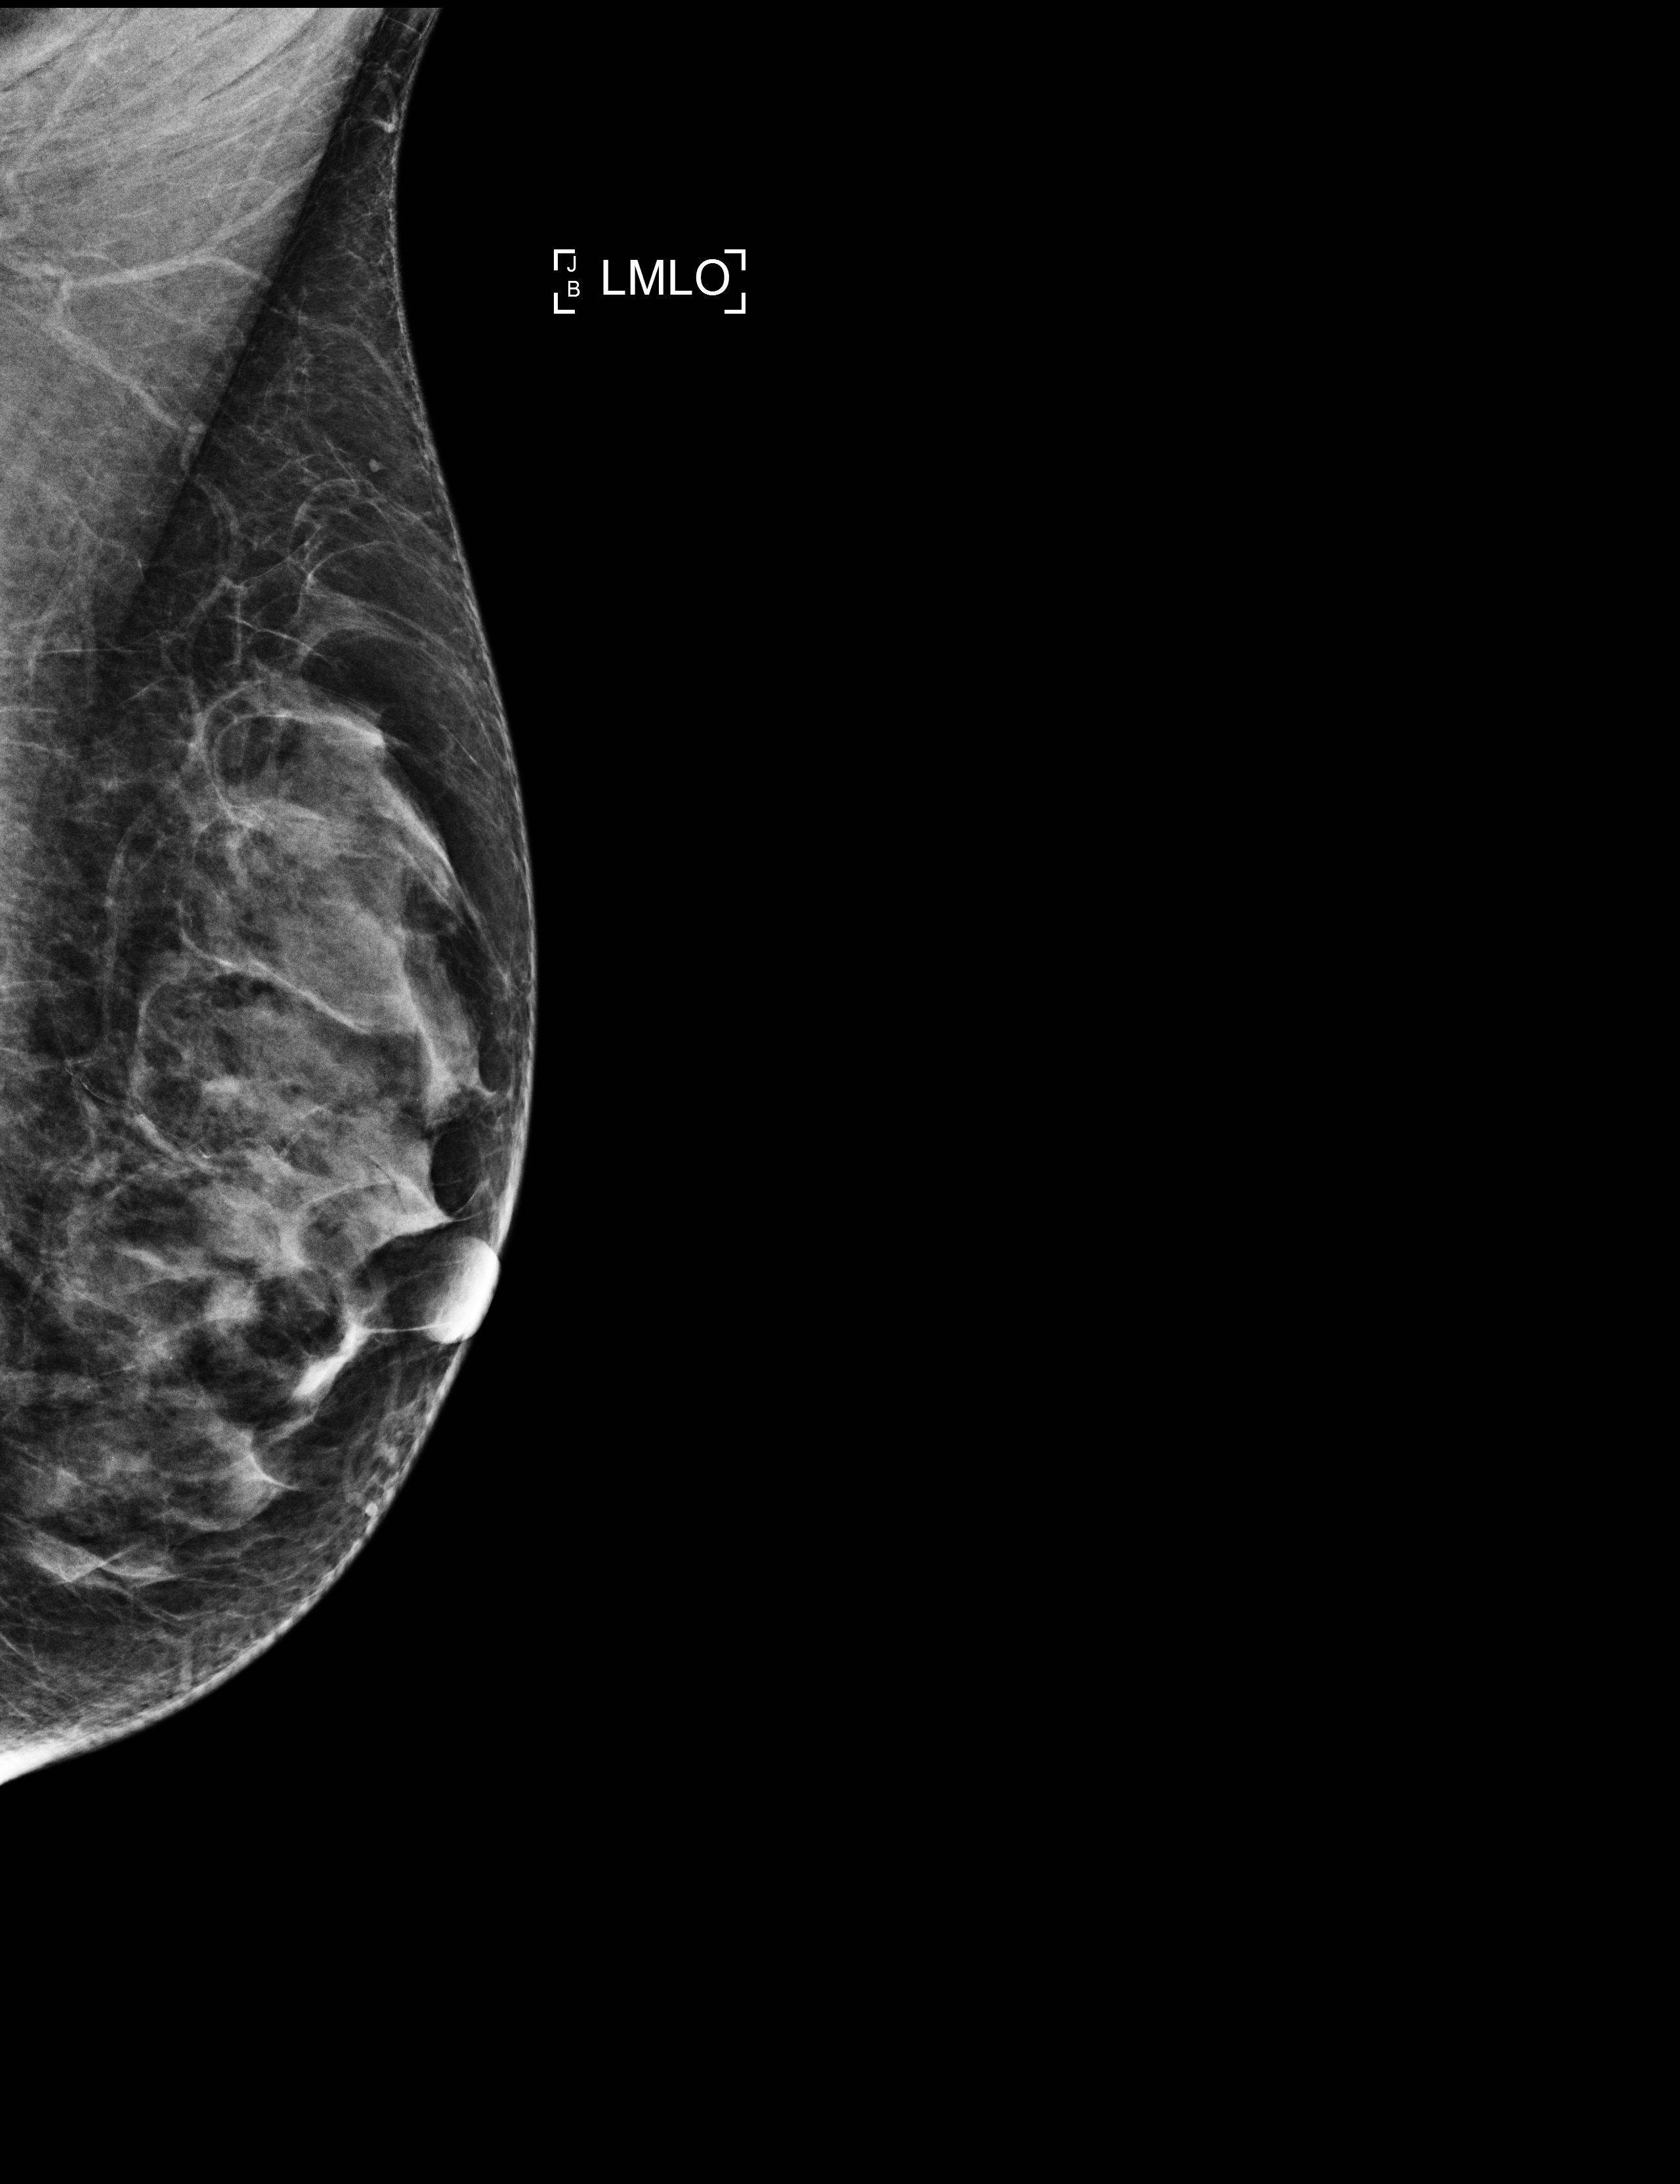
Digital mammogram (FFDM), left breast, medio-lateral oblique projection, annual screening mammography examination, compressed breast thickness 38 mm, system: Selenia Dimensions. Patient aged 58 years (female).
Breast density at the screening exam (both breasts): heterogeneously dense (BI-RADS density category c). Final BI-RADS category for the screening round (tomosynthesis exam, both breasts): category 1. Recall: no recall after this screen.